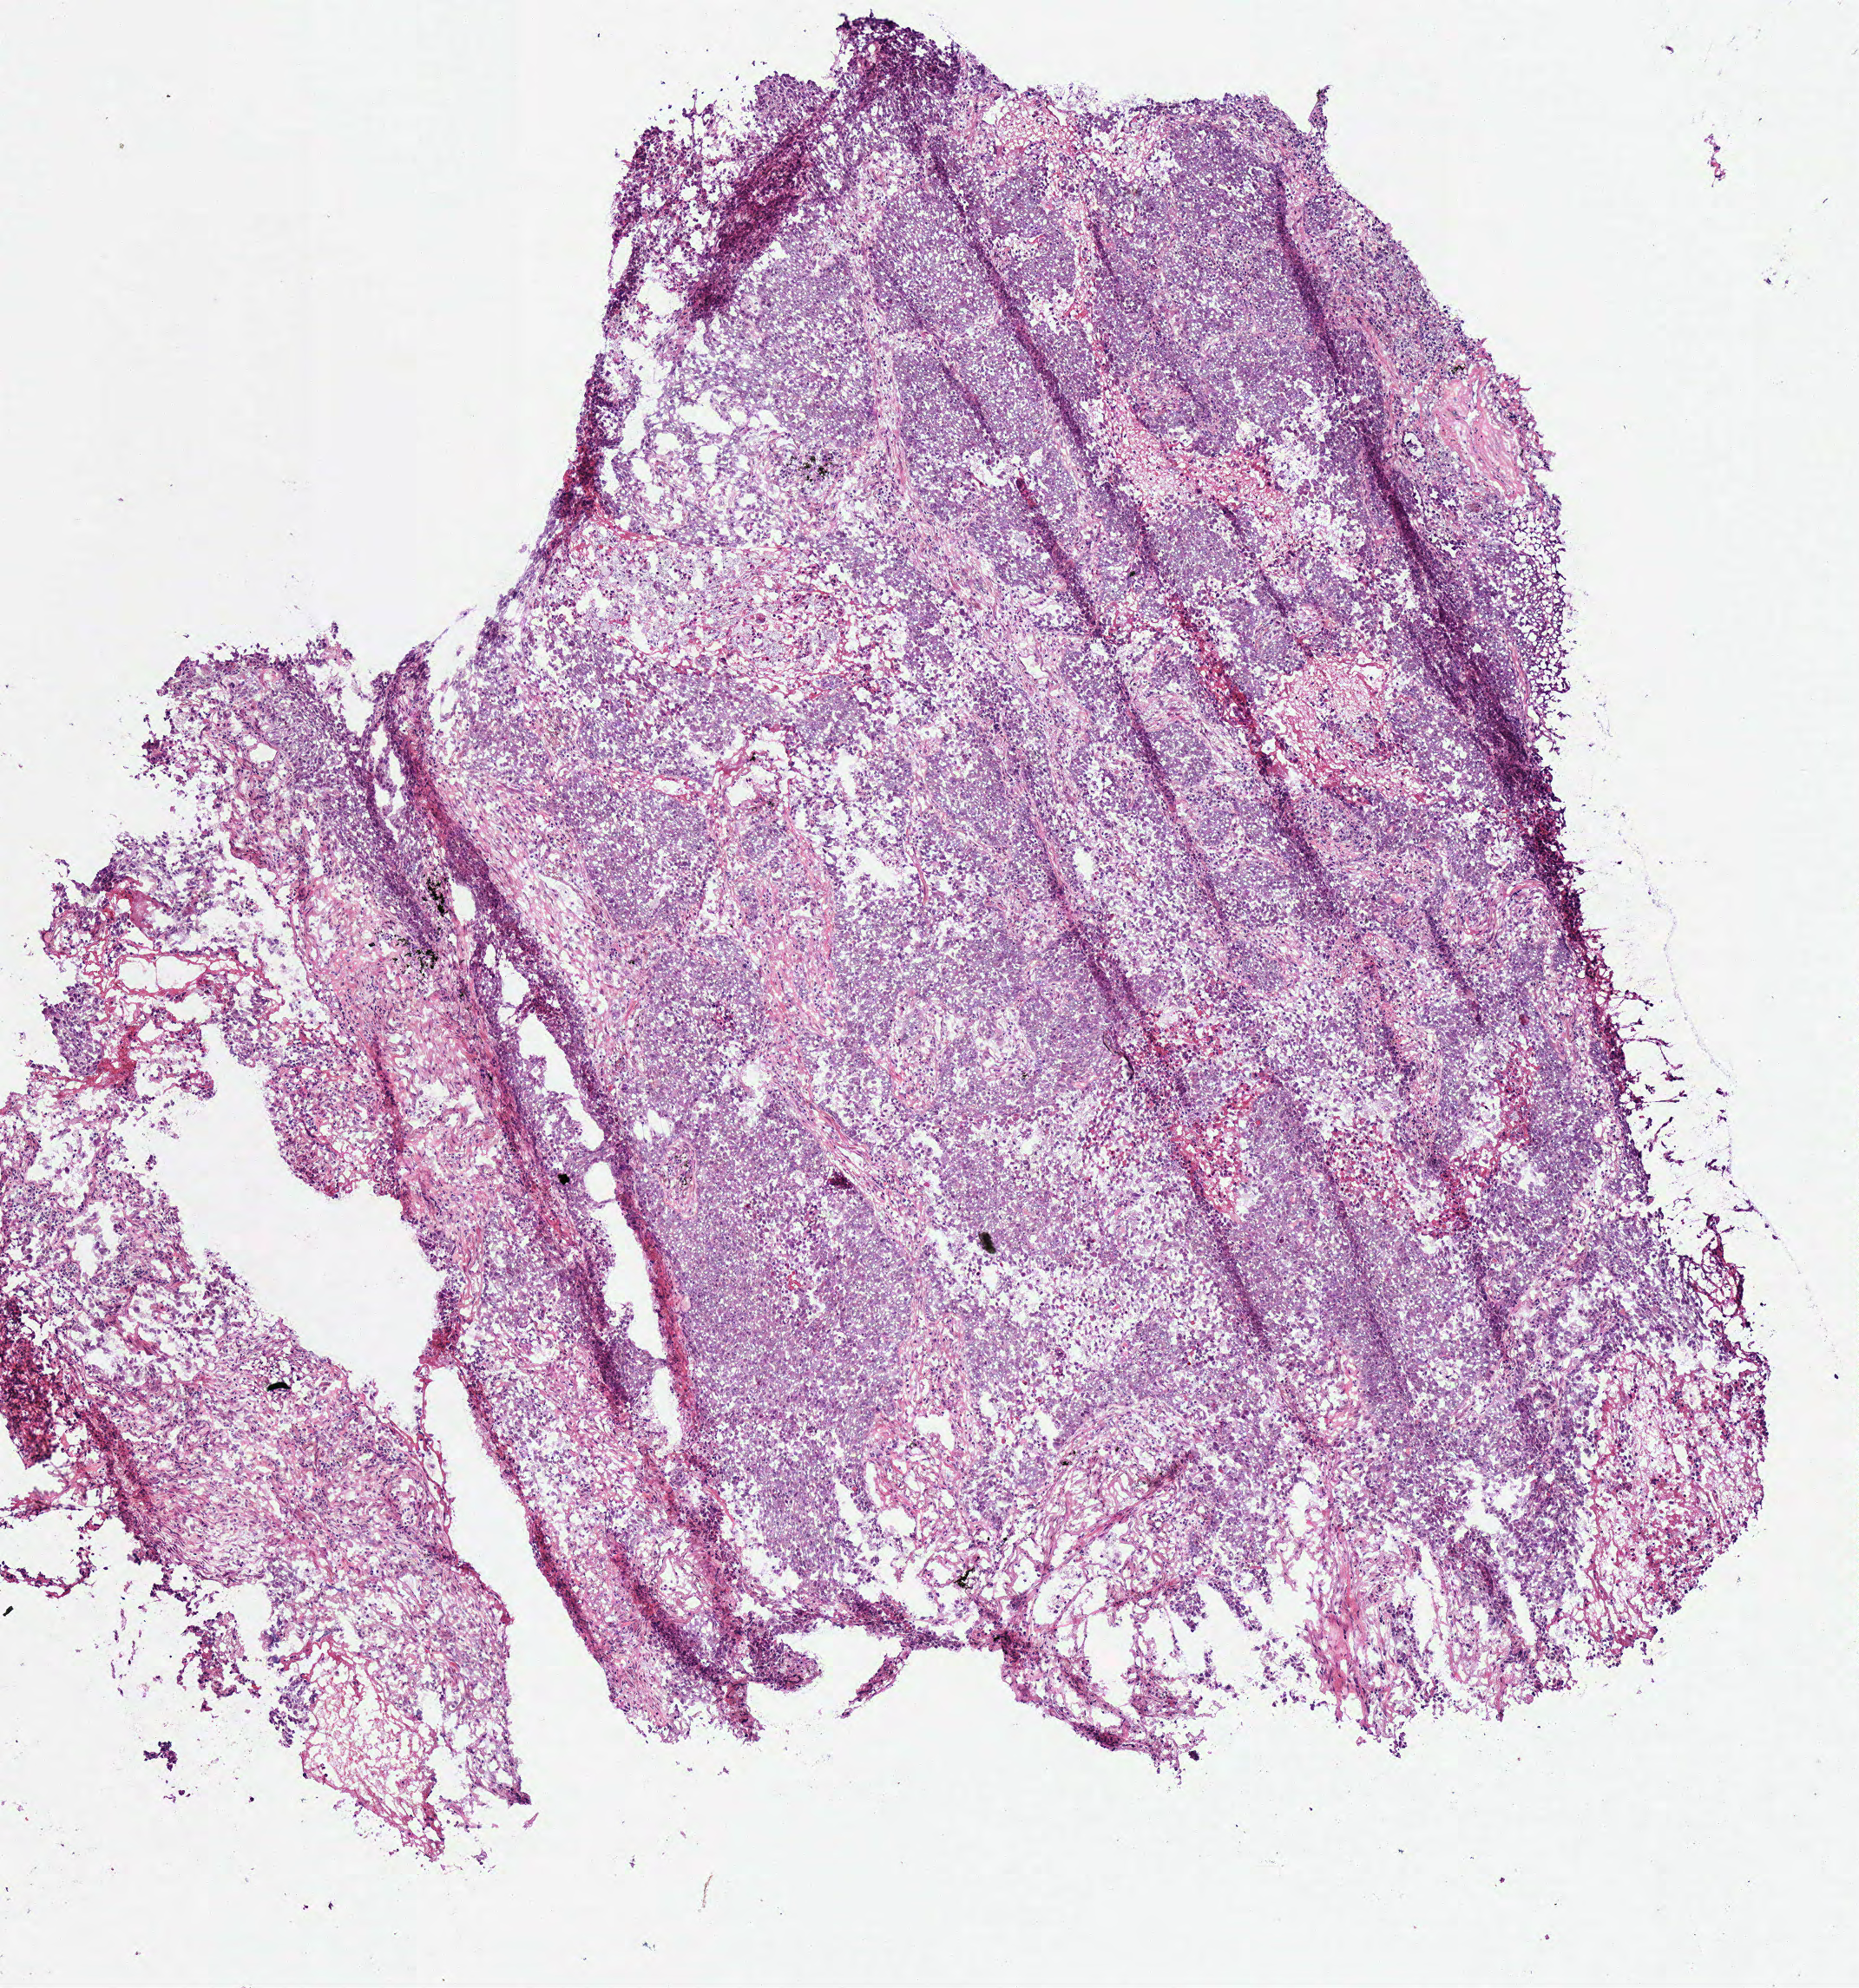
H&E-stained whole-slide image — a low-resolution overview of the entire scanned area, about 4.2 x 4.5 mm. Frozen section from the top of the tissue portion. Primary tumour sample from the lung. Female, age 72 years at initial diagnosis. Slide review estimates, as recorded: tumour cells 85%, tumour nuclei 95%, normal cells 0%, stromal cells 14%, necrosis 1%. Infiltration values recorded for this section: lymphocyte infiltration 1%.
* diagnosis: Squamous cell carcinoma, NOS (upper lobe, lung)
* AJCC pathologic stage: I (6th edition)